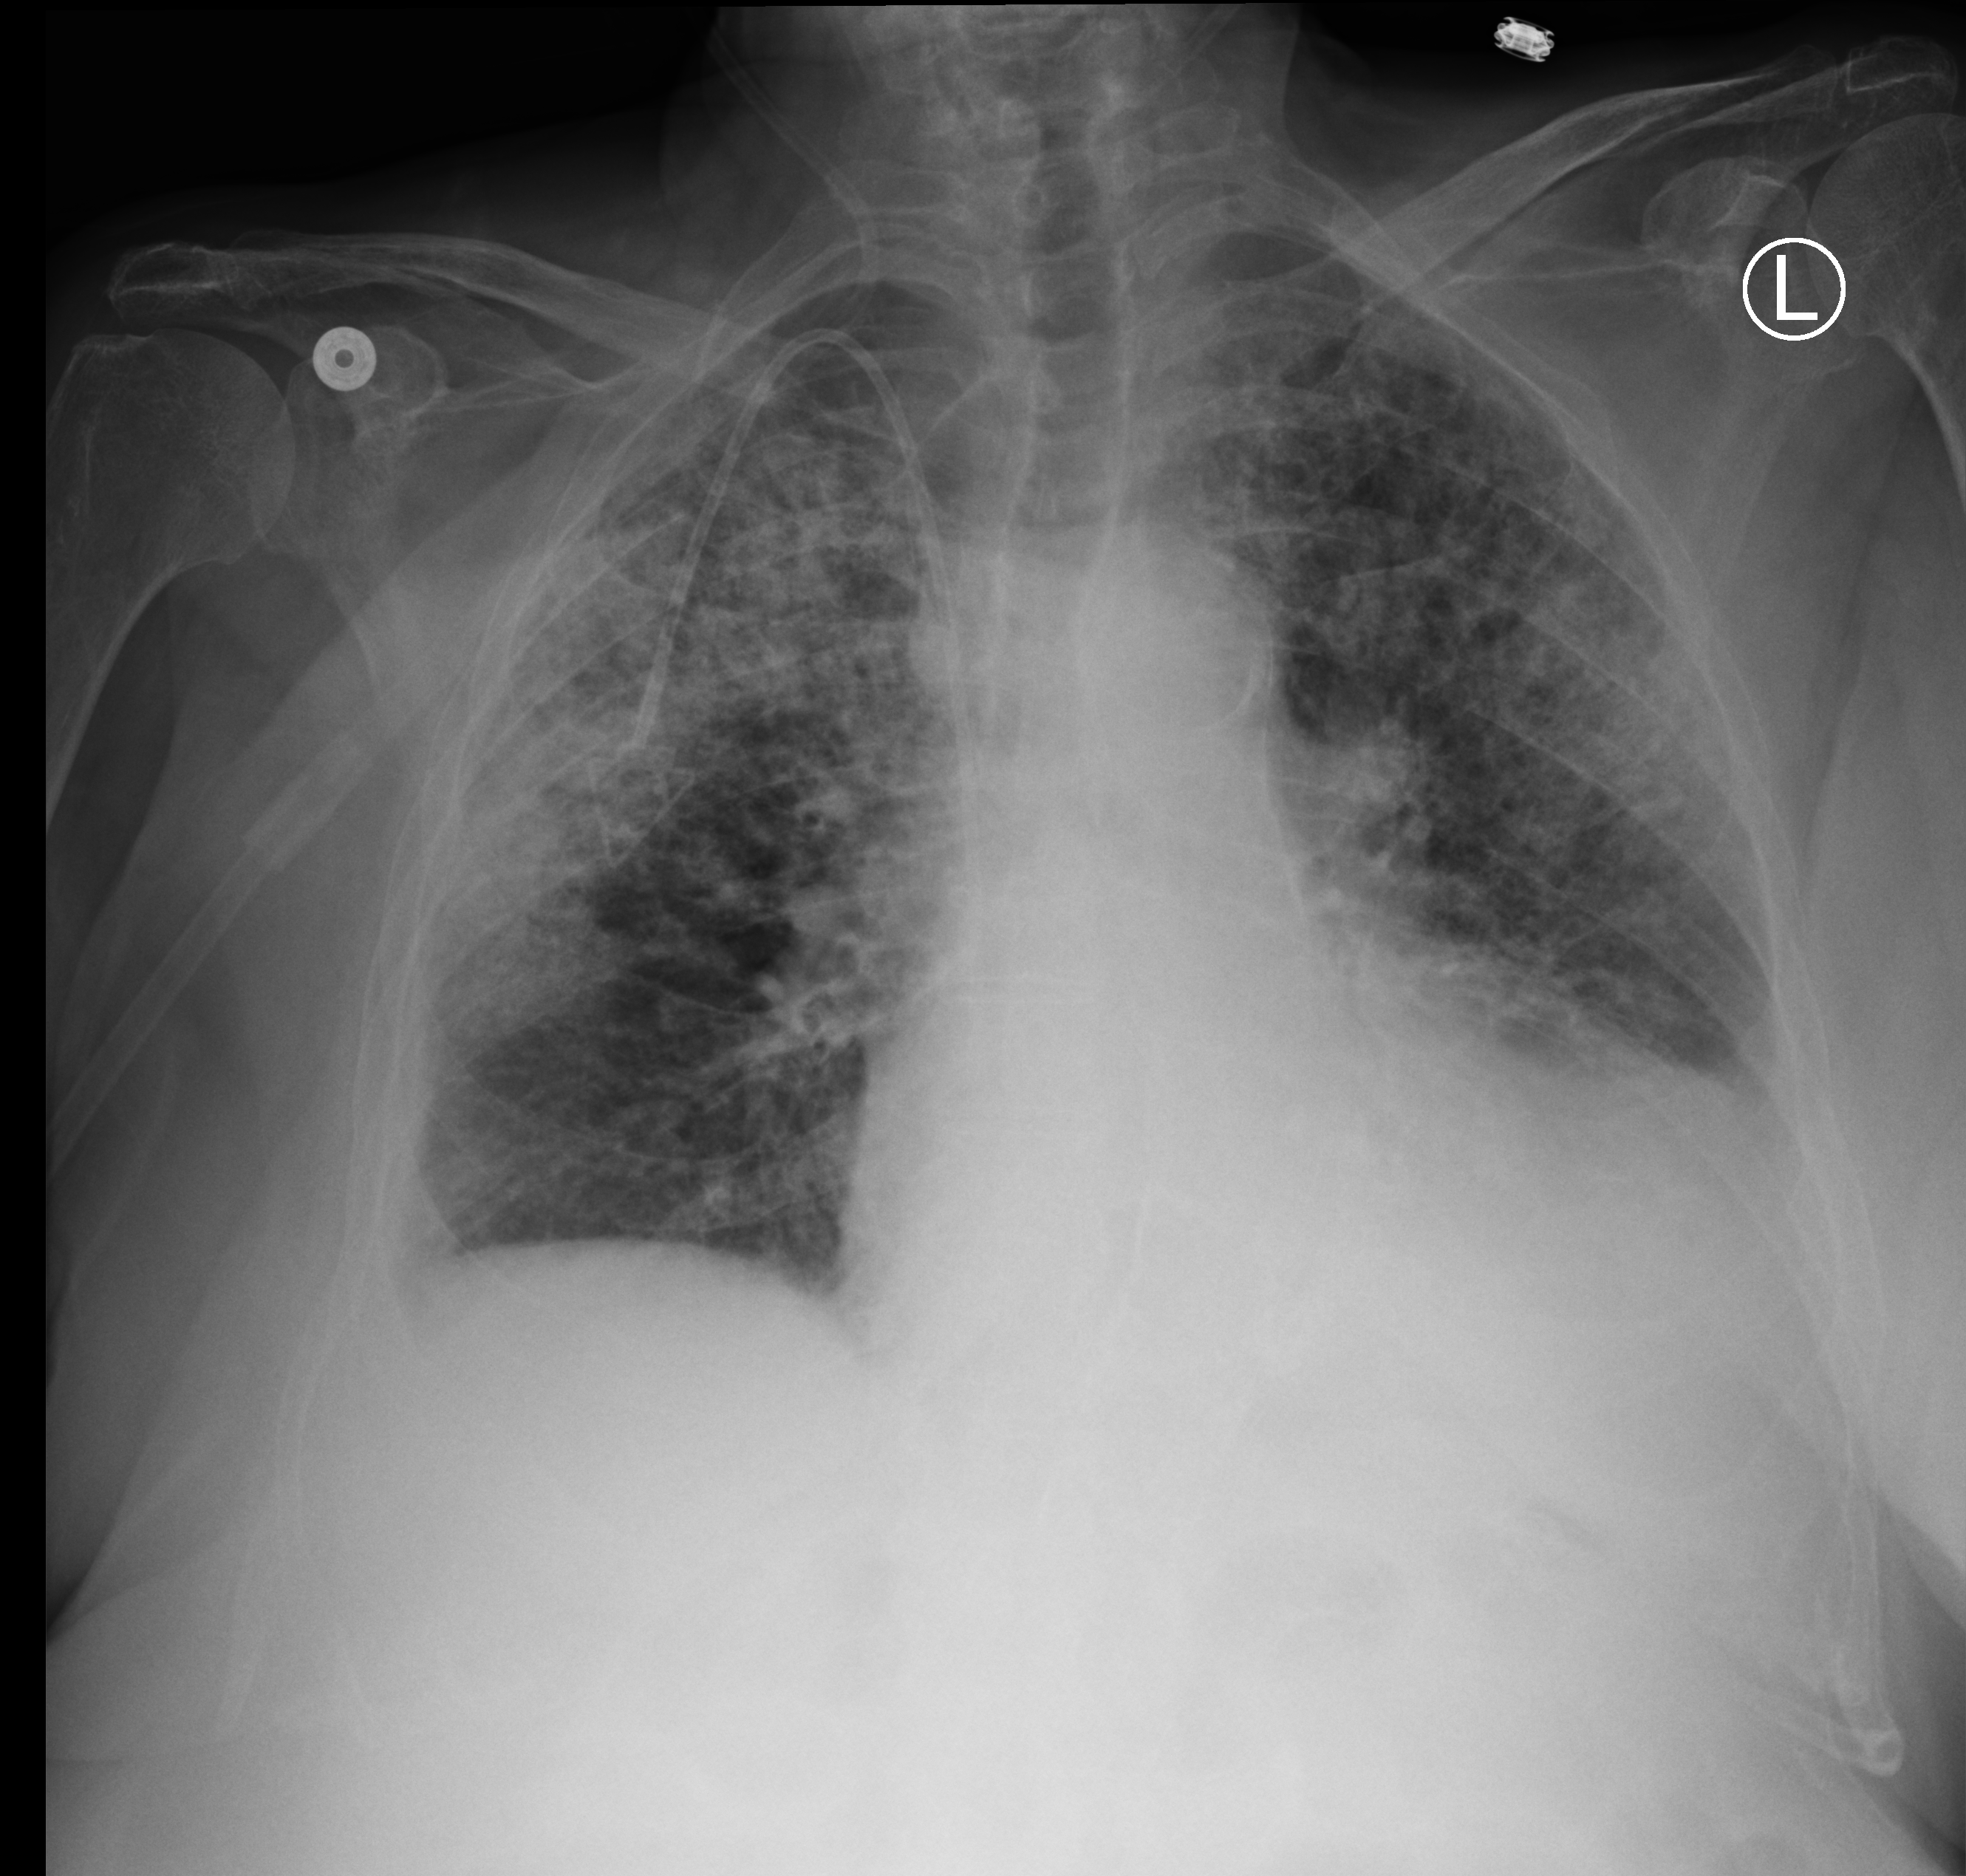
Bedside chest radiograph (computed radiography); anteroposterior (AP) projection. Patient hospitalised with COVID-19; female, aged 75–90 years.
Hospital-stay facts (about this admission, not read from this image; timing relative to this image not recorded): diabetes (admission record): no; length of hospital stay: 16 days; hypertension (admission record): yes.